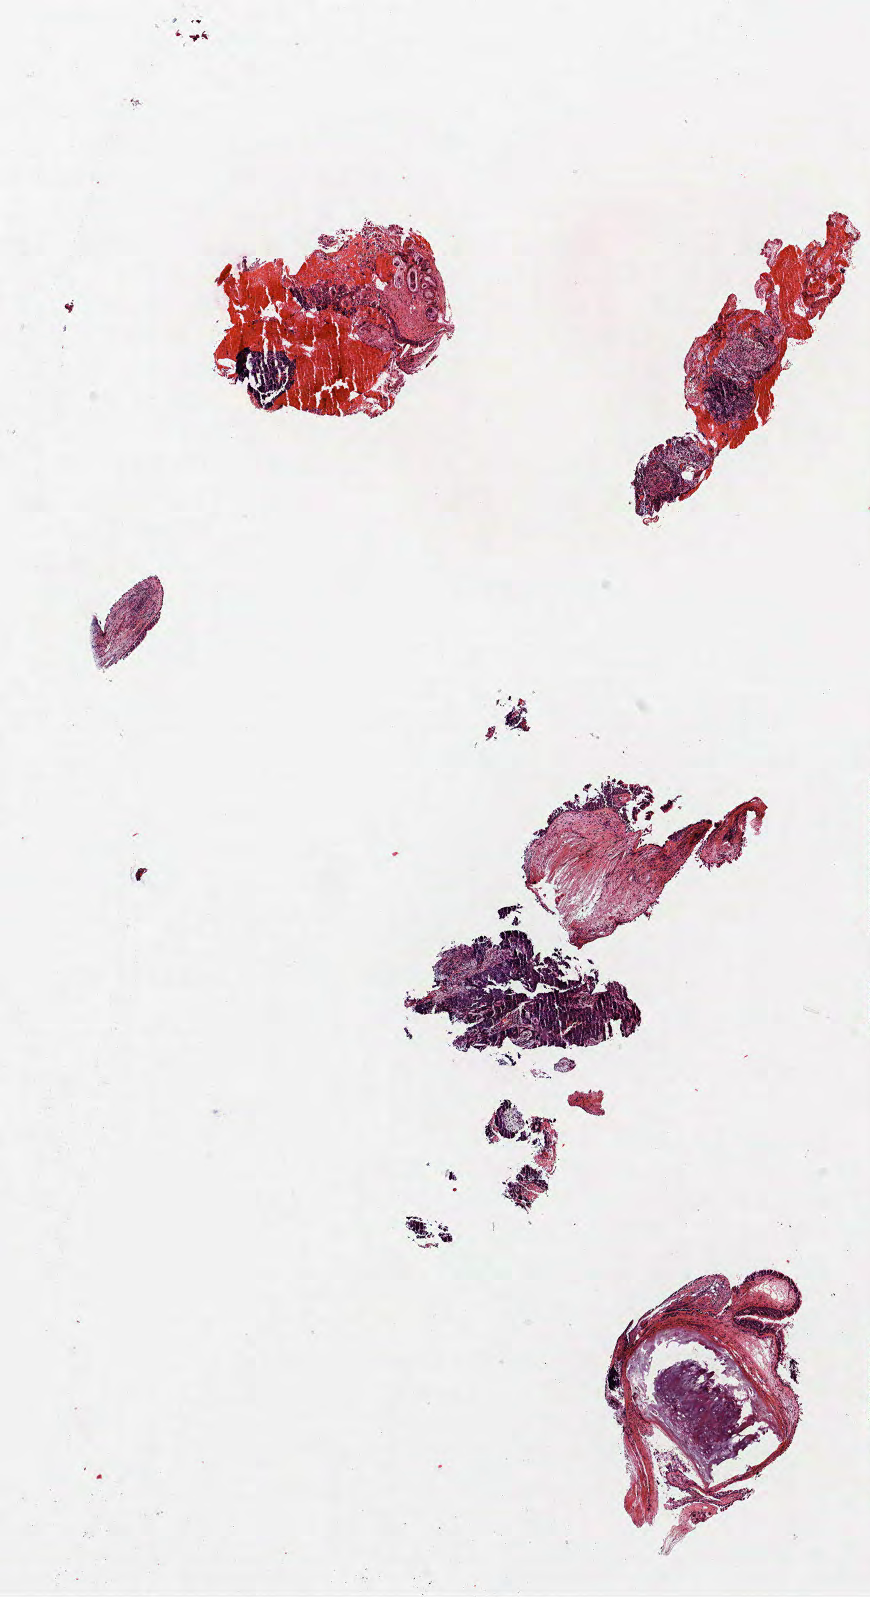
Whole-slide histology image, H&E-stained — low-resolution overview of the scanned area, about 7.0 x 12.8 mm. Formalin-fixed paraffin-embedded (FFPE) section. Lung tissue. Male, age 69 at enrolment. Former smoker at enrolment. Grade: poorly differentiated (G3).
Primary tumour location (clinical record): left upper lobe. Participant's lung-cancer diagnosis: Non-small cell carcinoma. Tumour size (pathology): 100 mm. Stage (AJCC 6th edition): IB.